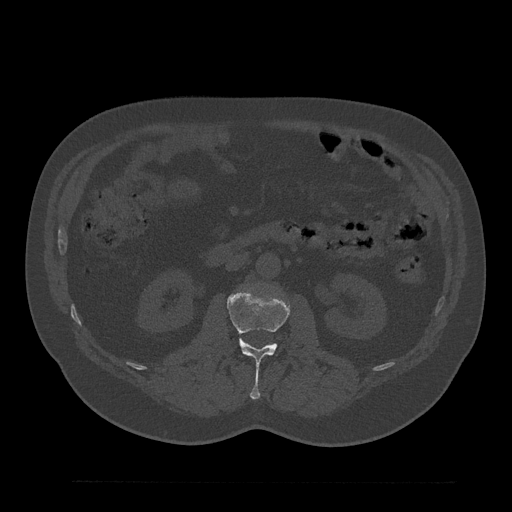
CT including the spine, one axial slice; slice 92 of 797 in the series (ordered by position); 120 kVp; bone window (W 1800 / L 400 HU); 0.5 mm slice thickness; 512 × 512 image matrix, field of view 430 × 430 mm. Patient: male, 61 years. From the clinical record (not read from this slice): primary cancer: prostate.
Annotated regions visible in this slice (semi-automatic segmentation, software-assisted and operator-edited):
- L2 vertebra: box from (x=227, y=287) to (x=290, y=399) px